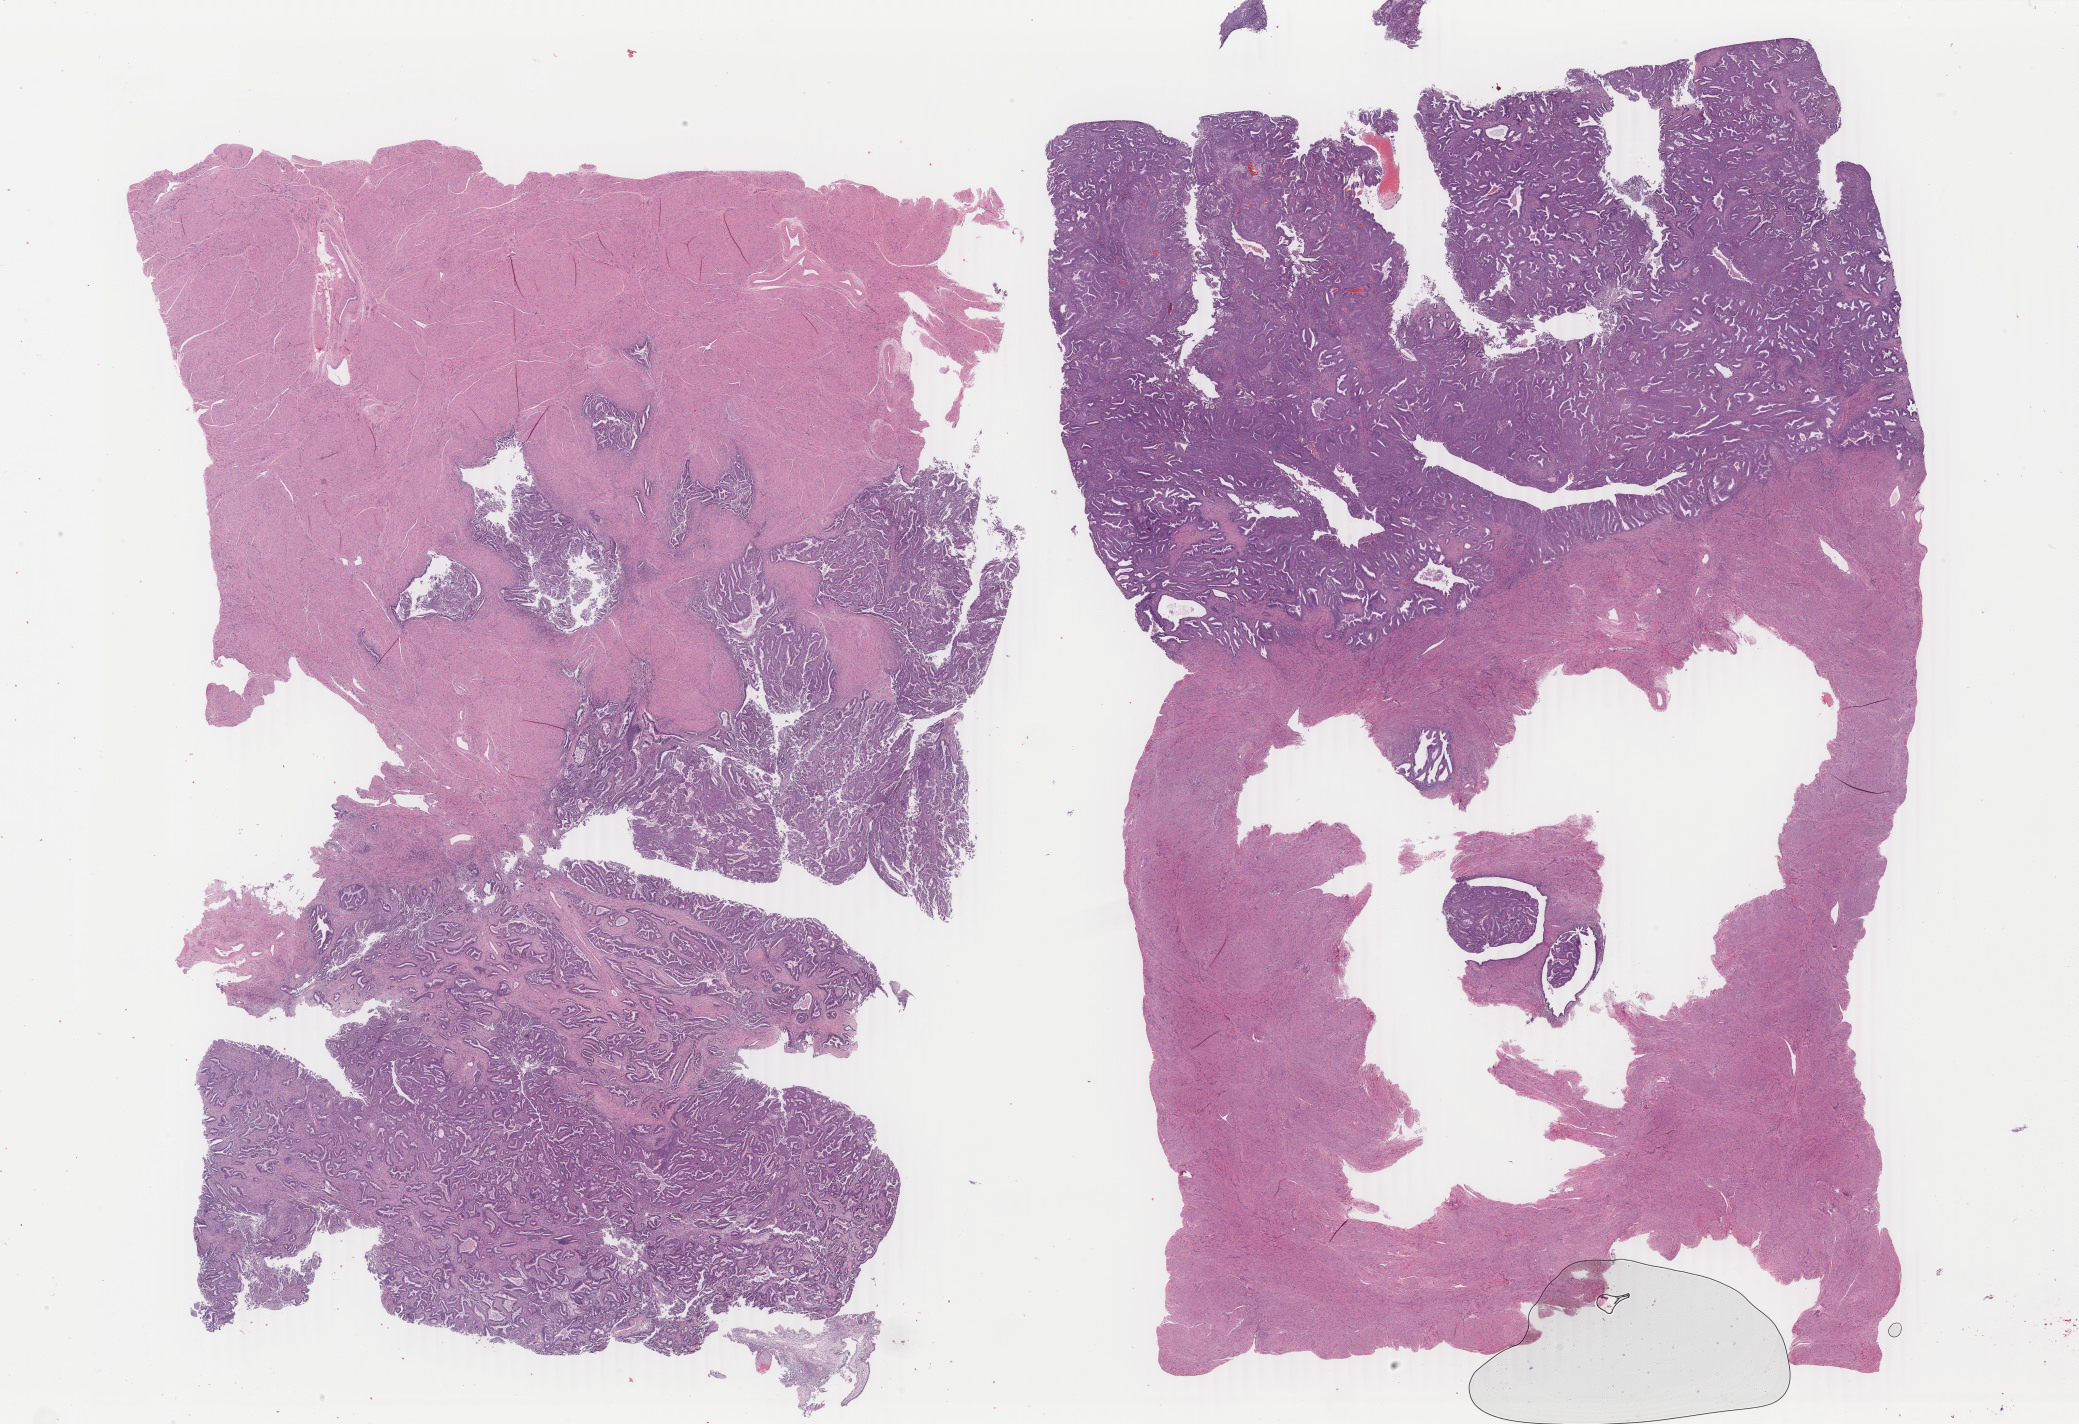
Digitized H&E tissue section (whole slide), shown as a low-resolution overview of the whole scanned area (about 33.1 x 22.7 mm, acquisition: 40x scan). Formalin-fixed paraffin-embedded (FFPE) diagnostic section. Uterus, primary tumour sample. Patient: female, age at initial diagnosis 39 years. Histologic grade: G1 (well differentiated).
FIGO stage: IA. Diagnosis: Endometrioid adenocarcinoma, NOS (endometrium).